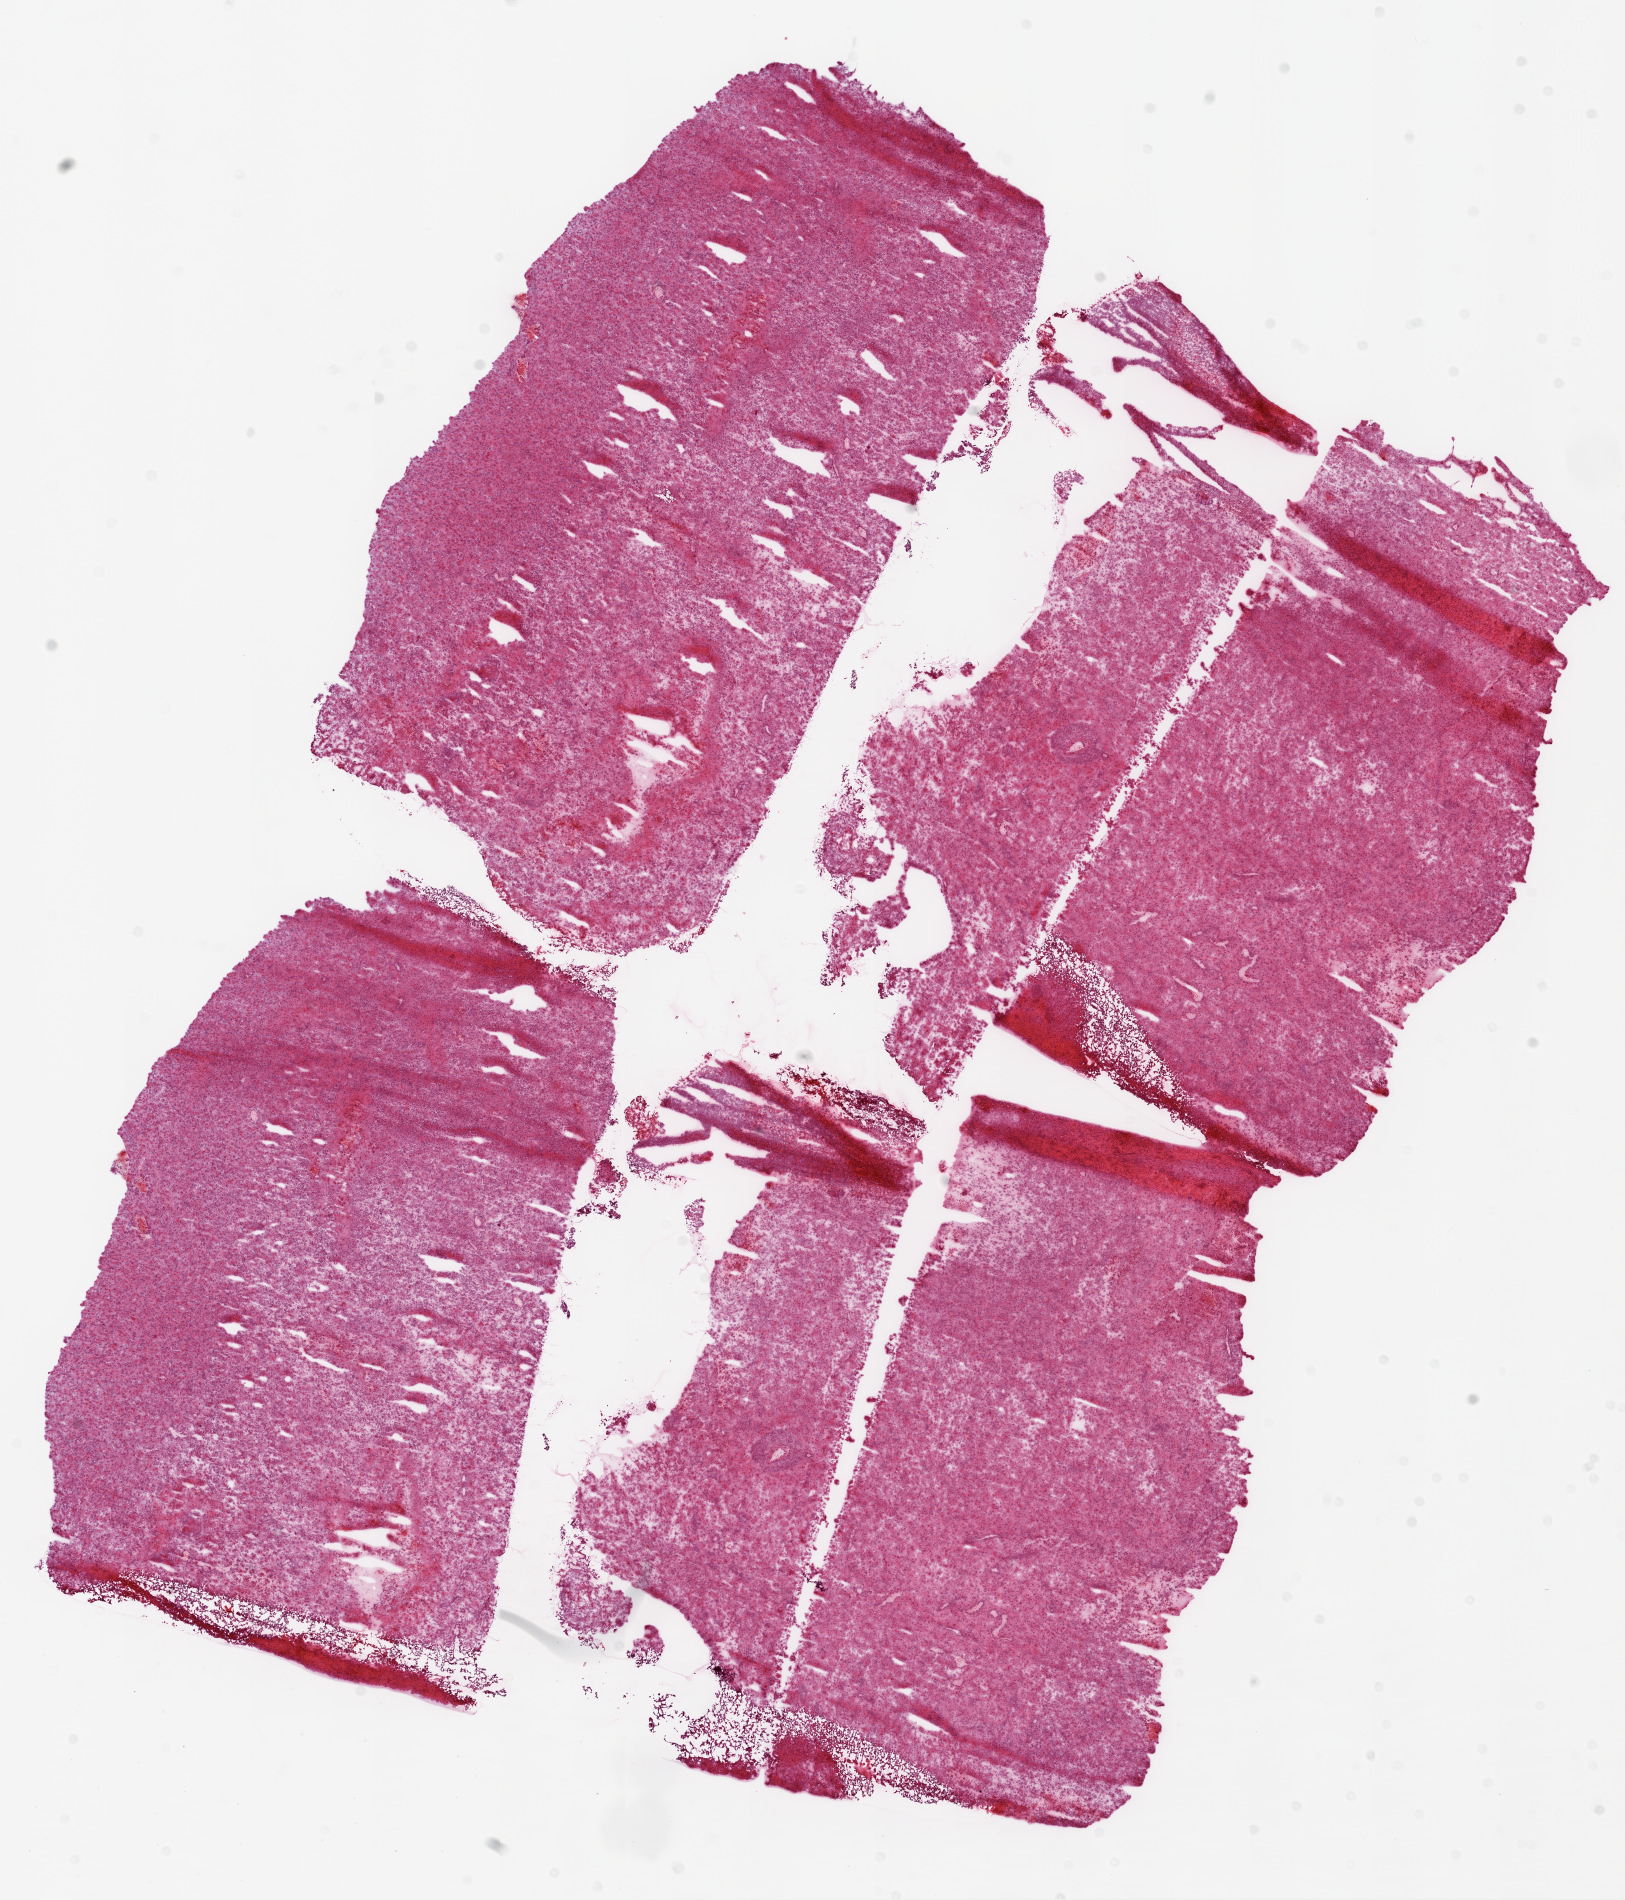
Digitized H&E tissue section (whole slide) — a low-resolution overview of the entire scanned area, about 13.0 x 15.2 mm (from a 20x scan). Frozen section from the top of the tissue portion. Sample: primary tumour, brain. Female patient; age at initial diagnosis 49 years. Slide review estimates, as recorded: tumour cells 95%, tumour nuclei 95%, normal cells 0%, stromal cells 0%, necrosis 5%.
Pathologic diagnosis: Glioblastoma.